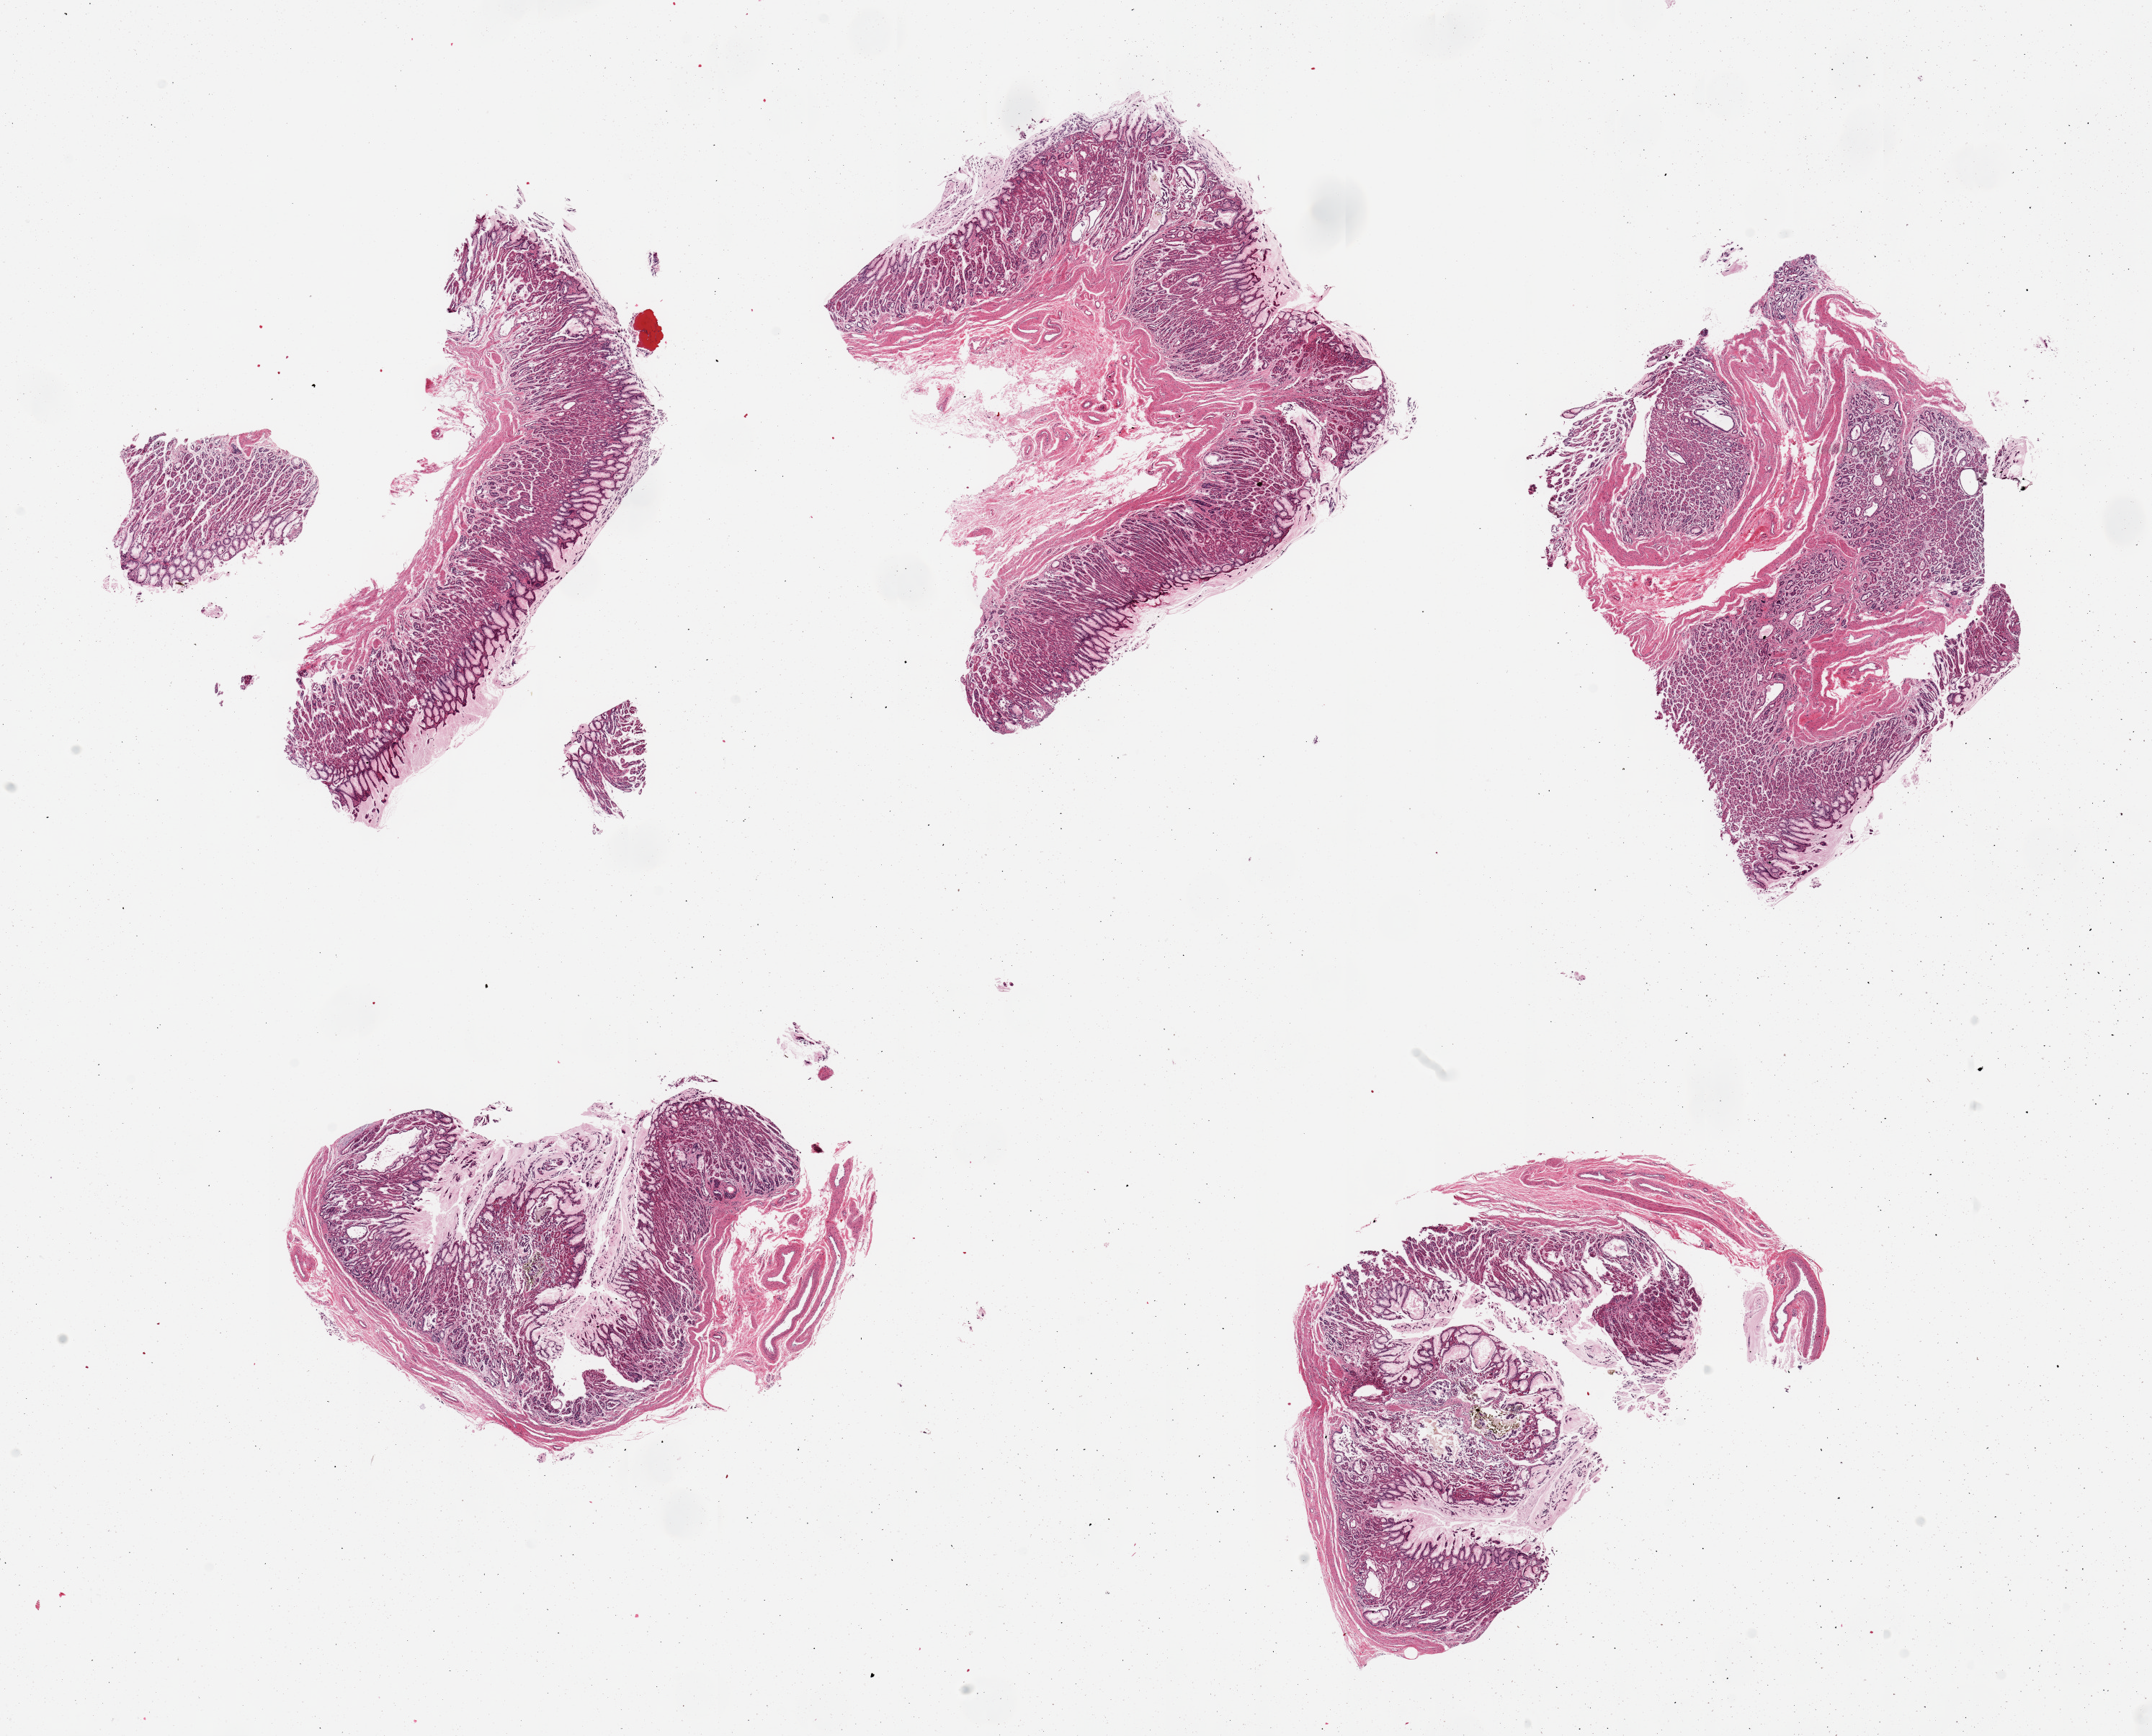
Digitized haematoxylin and eosin-stained section, brightfield — low-resolution overview of the scanned area, about 23.6 x 19.1 mm. PAXgene-fixed, paraffin-embedded tissue. Target tissue: stomach. Tissue donor sample. Donor sex: male.
- pathologist's review note for this sample: 5 pieces; mucosa only, no muscularis; focal gastric contents mainly in 2 pieces